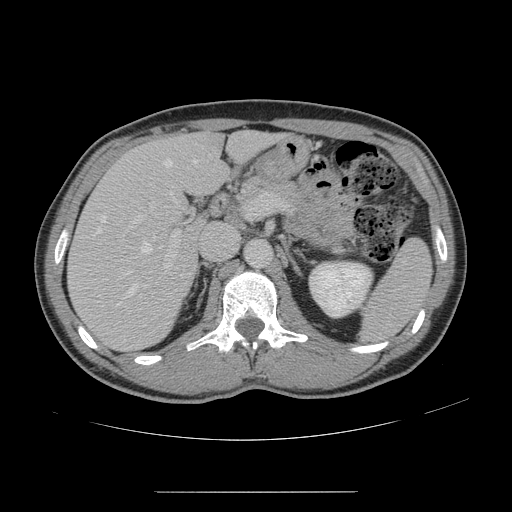
Contrast-enhanced abdominal CT, one axial slice; position 85 of 178 along the scan axis; 120 kVp; intravenous contrast given; soft-tissue window (W 400 / L 40 HU); 2.5 mm slice thickness; 512 × 512 image matrix, field of view 401 × 401 mm. Male patient, age 53 years. From the clinical record (not read from this slice): diagnosis: colorectal cancer liver metastases, imaged before liver resection; multiple liver metastases: yes.
Annotated regions visible in this slice (expert manual segmentation):
- hepatic veins: box from (x=95, y=159) to (x=197, y=307) px
- liver: (x=69, y=133)–(x=275, y=350)
- planned liver remnant (the part of the liver to remain after resection): (x=153, y=132)–(x=276, y=194)
- portal vein (with intrahepatic branches): (x=130, y=193)–(x=267, y=279)